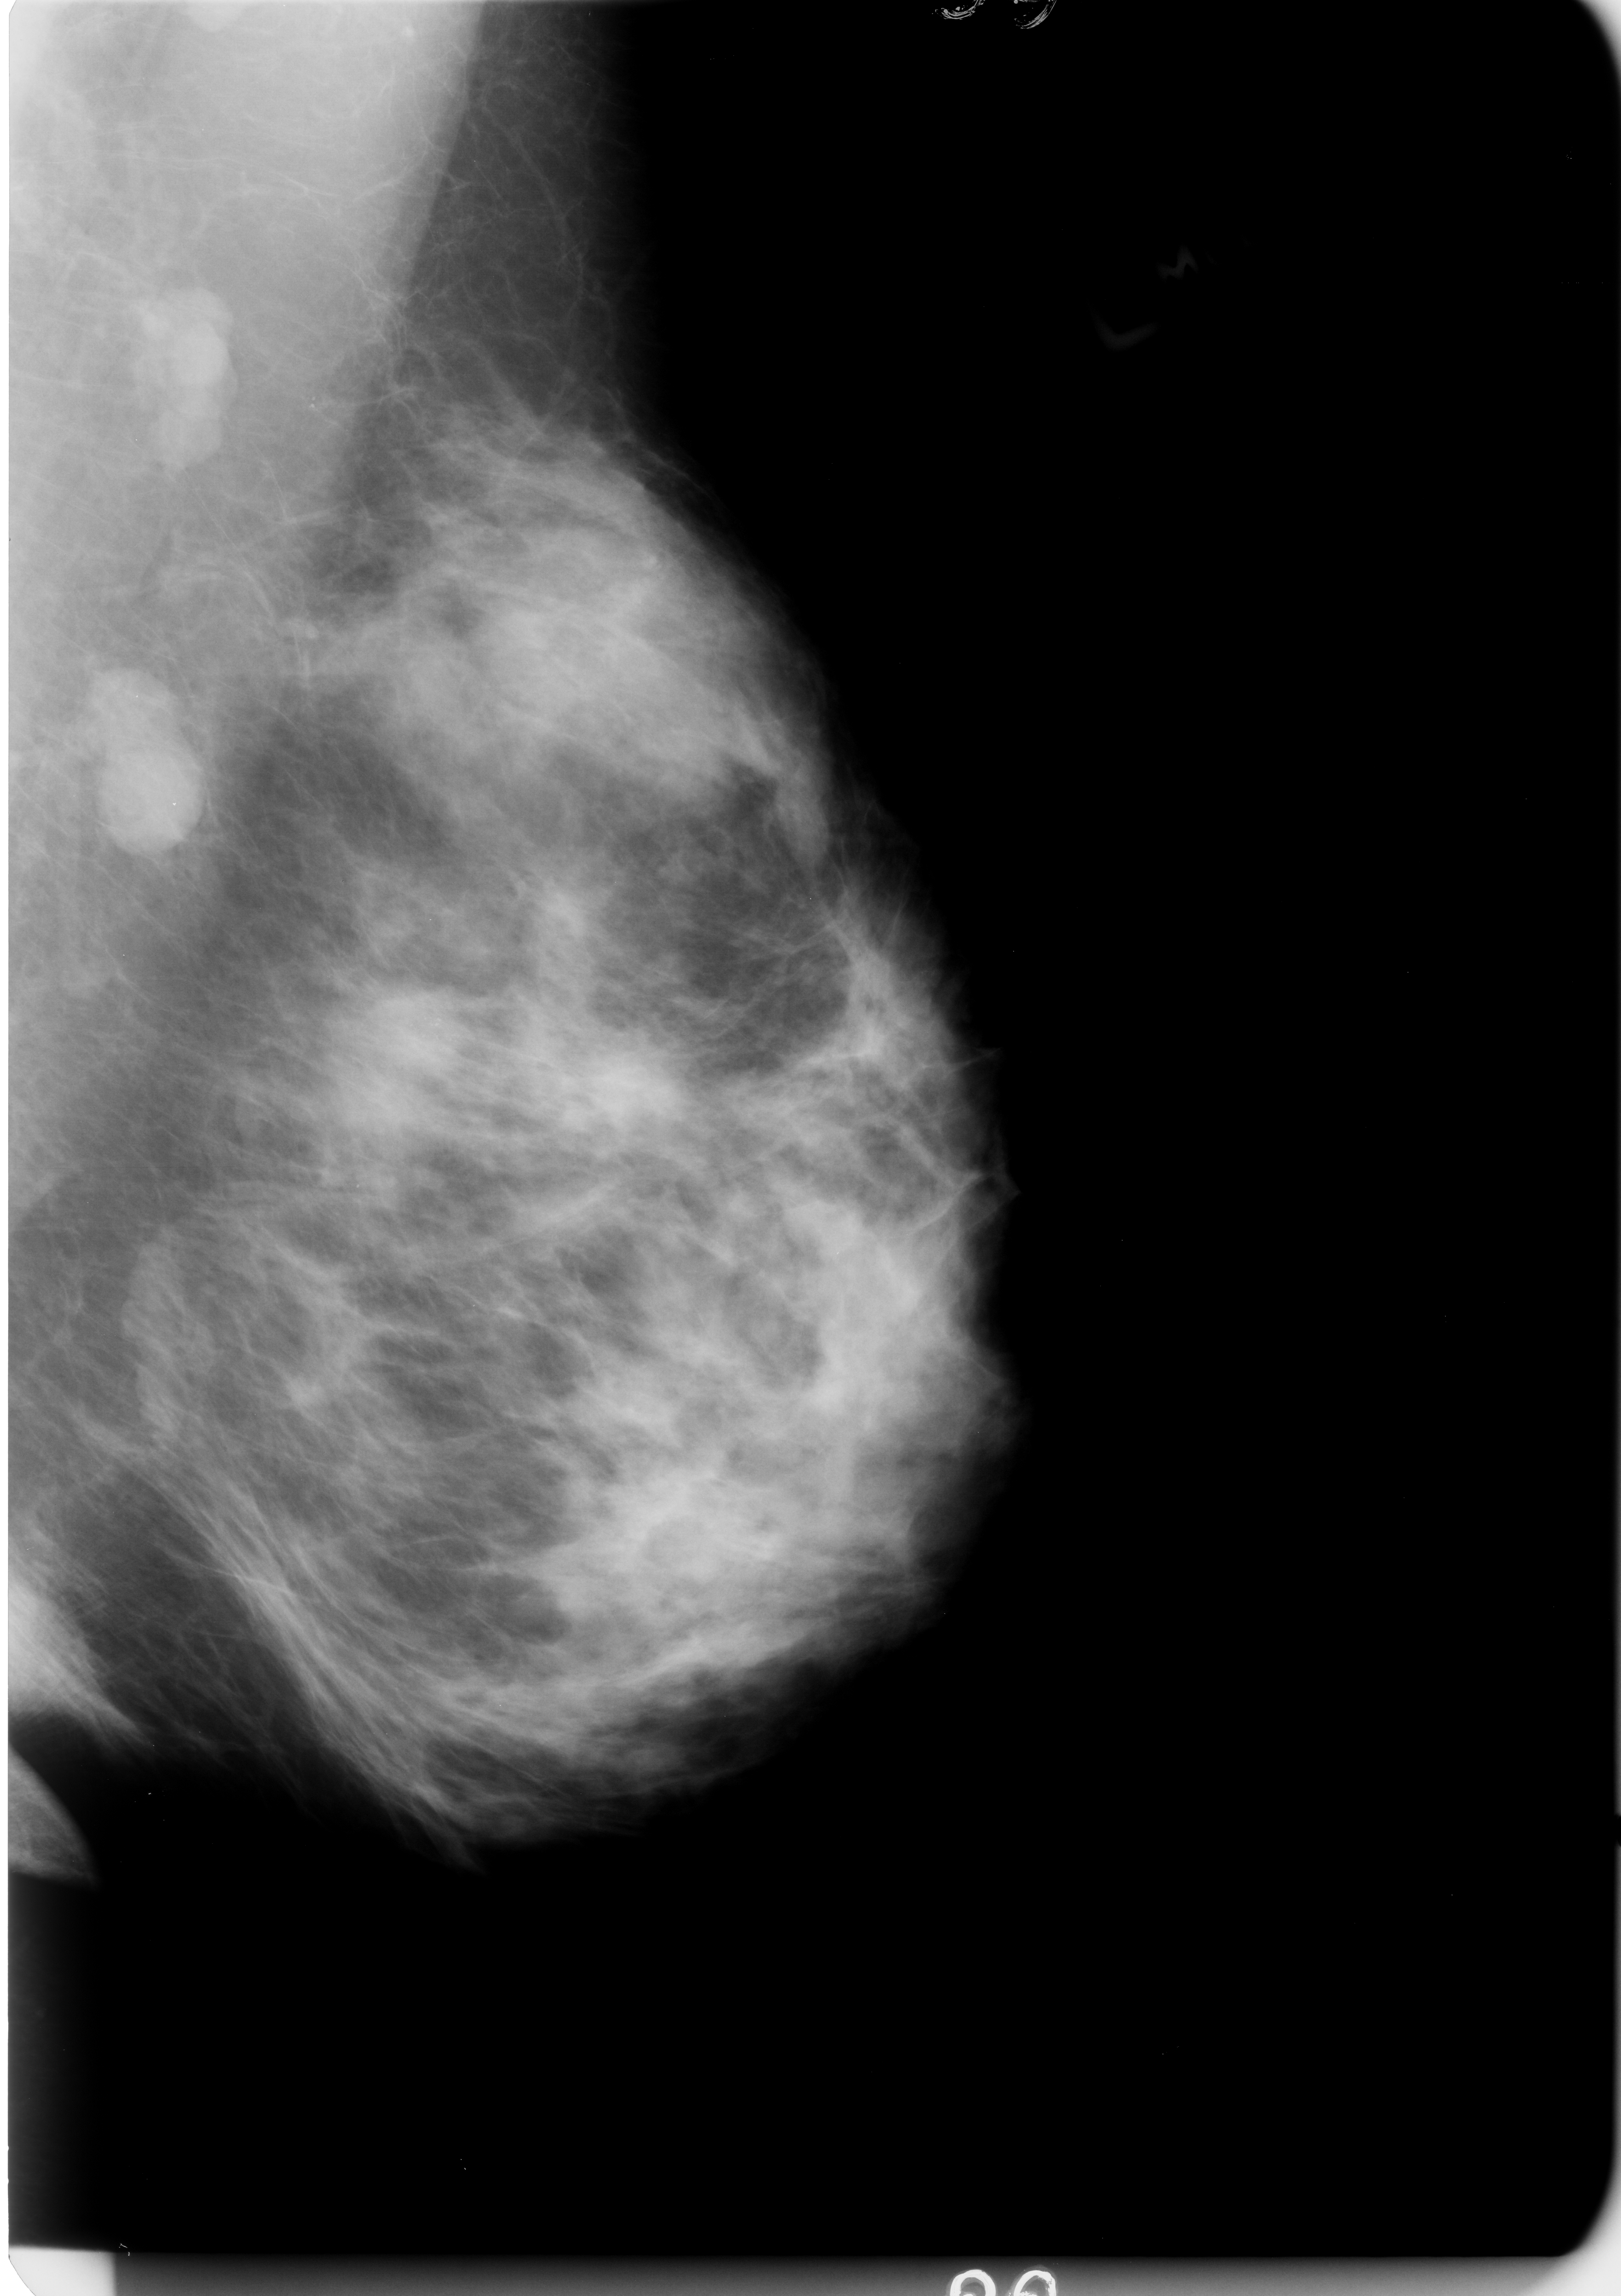
Mammogram (digitized film); left breast; MLO view; BI-RADS breast density category 3 (scale 1–4); 1621 × 2296 image matrix.
Expert-marked regions of interest on this image (one box per marked abnormality):
- calcifications, morphology pleomorphic, distribution clustered; BI-RADS assessment category 4; subtlety rating 3 on a 1 (subtle) to 5 (obvious) scale; pathology (as recorded): malignant: bounding box [x1, y1, x2, y2] px = [397, 990, 474, 1061]